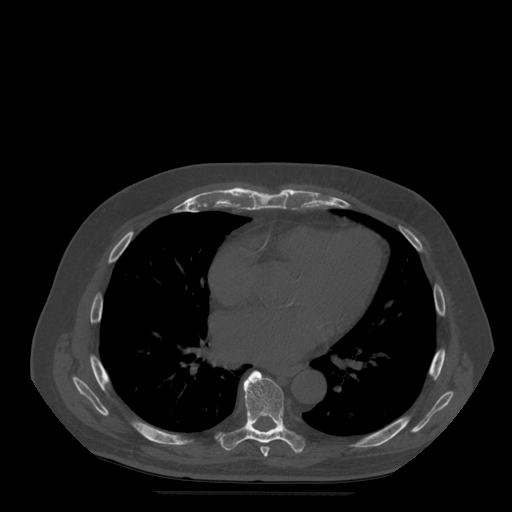
CT including the spine, one axial slice. Position 314 of 522 along the scan axis. Bone window (W 1800 / L 400 HU). 512 × 512 image matrix. Patient age 72 years. Case-level facts recorded for this patient, not image findings: primary cancer: prostate.
Structures marked on this image (semi-automatic segmentation, software-assisted and operator-edited):
- T7 vertebra: bounding box (x1, y1, x2, y2) in pixels: (260, 447, 270, 457)
- T8 vertebra: (219, 371, 305, 453)